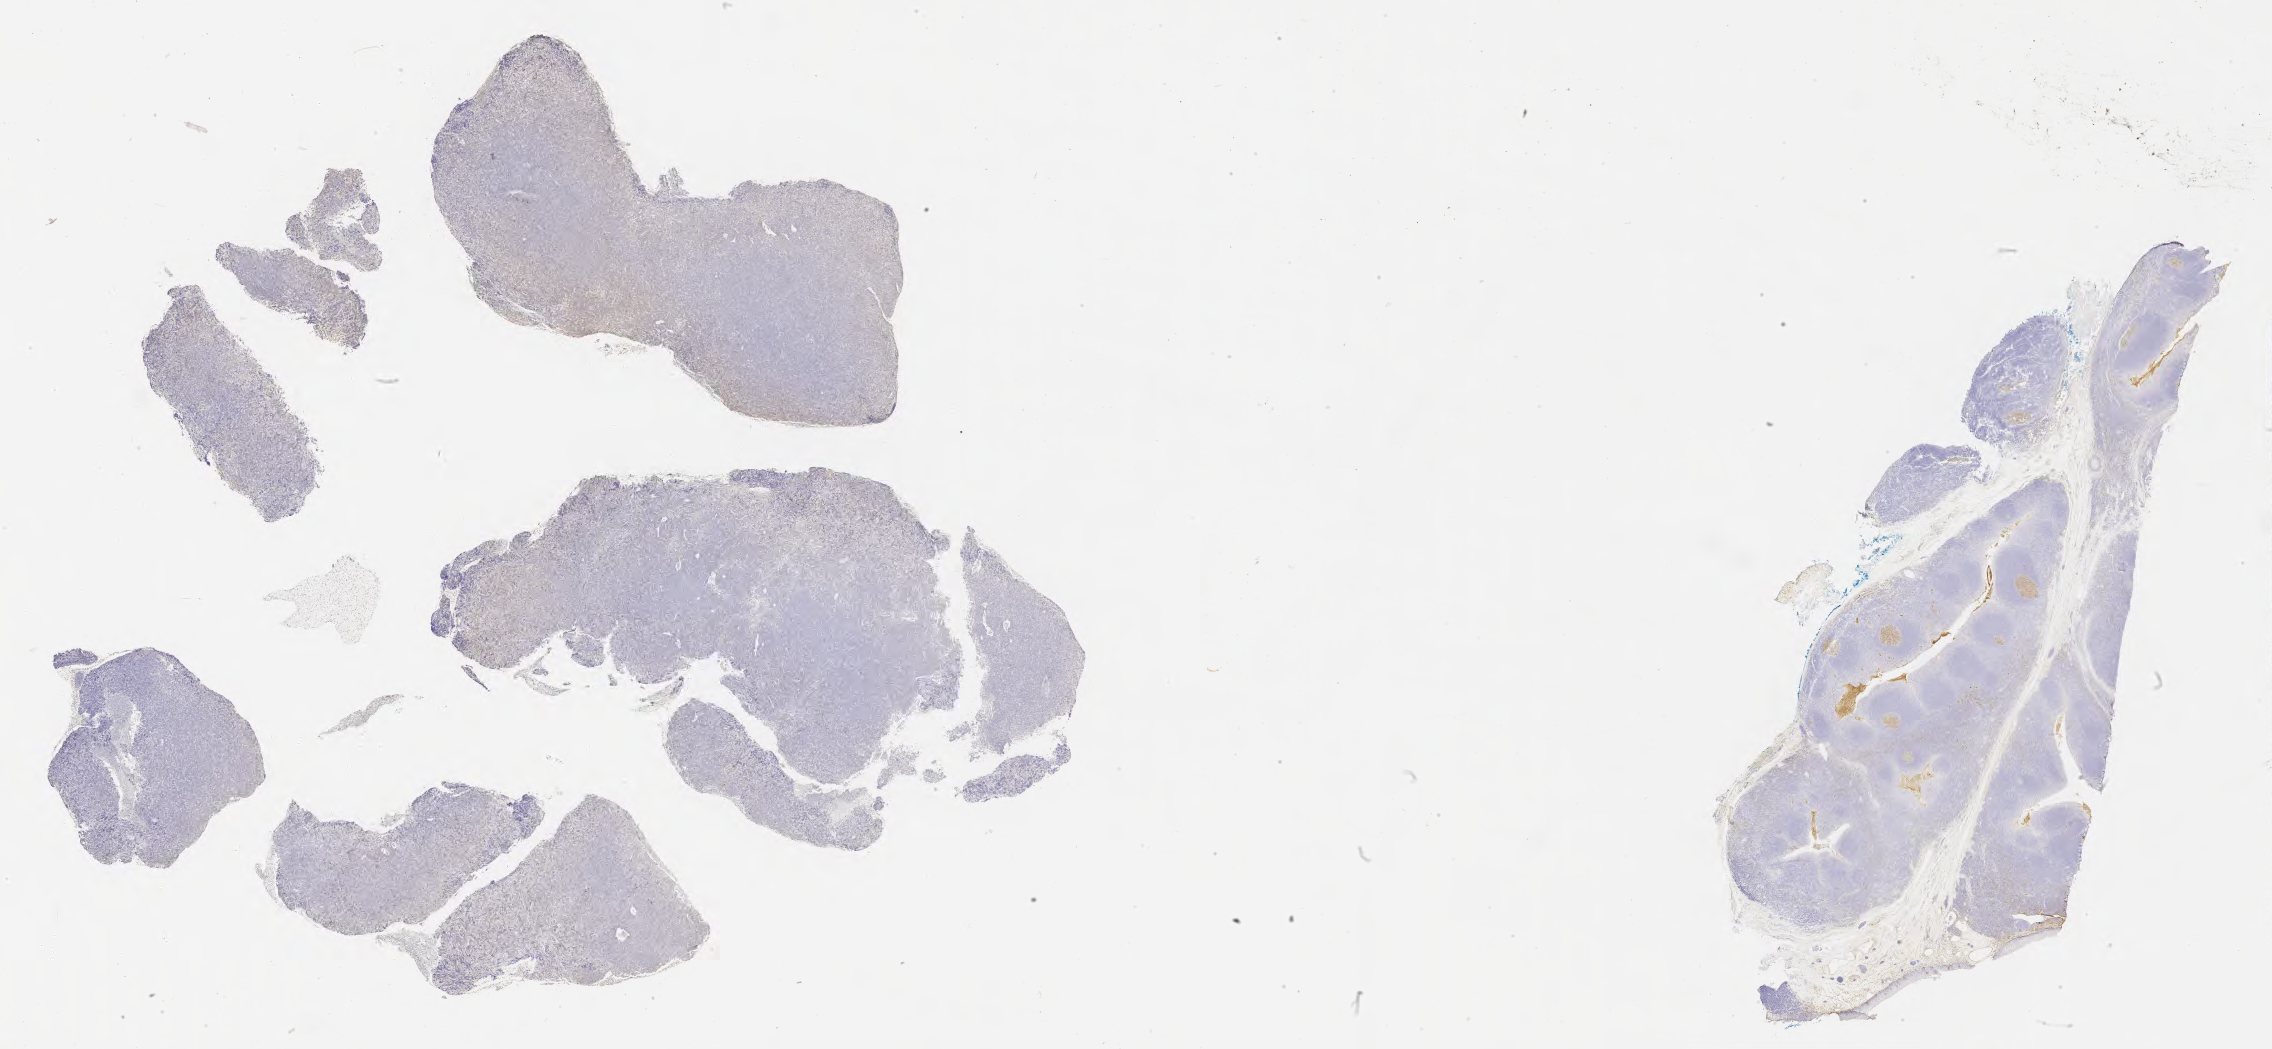
Whole-slide image, immunohistochemical stain for CD10 — whole scanned area (about 36.7 x 17.0 mm) shown as a low-resolution overview, tumor tissue, anatomic site: soft tissue. Female patient; age at initial diagnosis 9 years.
Diagnosis: Burkitt lymphoma, NOS.